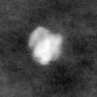
Crop from a digitized film mammogram around one marked abnormality, right breast, CC view.
Marked abnormality: calcifications, morphology coarse / round and regular / lucent center; BI-RADS assessment category 2; subtlety rating 4 on a 1 (subtle) to 5 (obvious) scale; benign without callback (not worked up further).